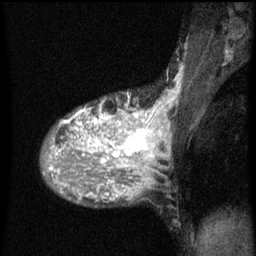
Breast MRI (dynamic contrast-enhanced), one sagittal slice. Slice 36 of 60 in the series (ordered by position). Dynamic contrast-enhanced series, image 2 of 3 at this slice position (ordered by acquisition). 1.5 T. TE 4.2 ms, TR 8 ms. 2 mm slice thickness. 256 × 256 image matrix, field of view 180 × 180 mm. Female patient, age 36 years.
Outlined on this slice (semi-automatic segmentation, software-assisted and operator-edited):
- analysis volume of interest (the breast-tissue region the enhancement analysis was run in; not a lesion): box from (x=44, y=98) to (x=167, y=161) px
- tumour enhancement mask (voxels above the 70 % enhancement threshold inside the analysis volume of interest): (x=48, y=98)–(x=165, y=161)